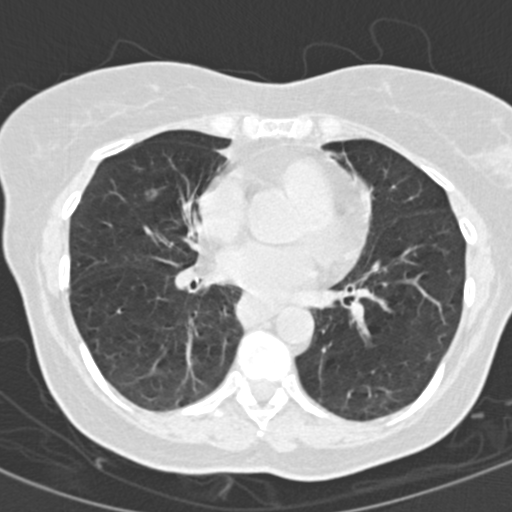
Low-dose screening chest CT, one axial slice; position 70 of 154 along the scan axis; reconstruction kernel B30f; 120 kVp; lung window (W 1500 / L -600 HU); 2 mm slice thickness; 512 × 512 image matrix.
Annotated regions visible in this slice (manually delineated by an expert):
- lesion 1 (nodule, middle lobe of right lung): bounding box <144,188,158,201> (left, top, right, bottom; pixels)